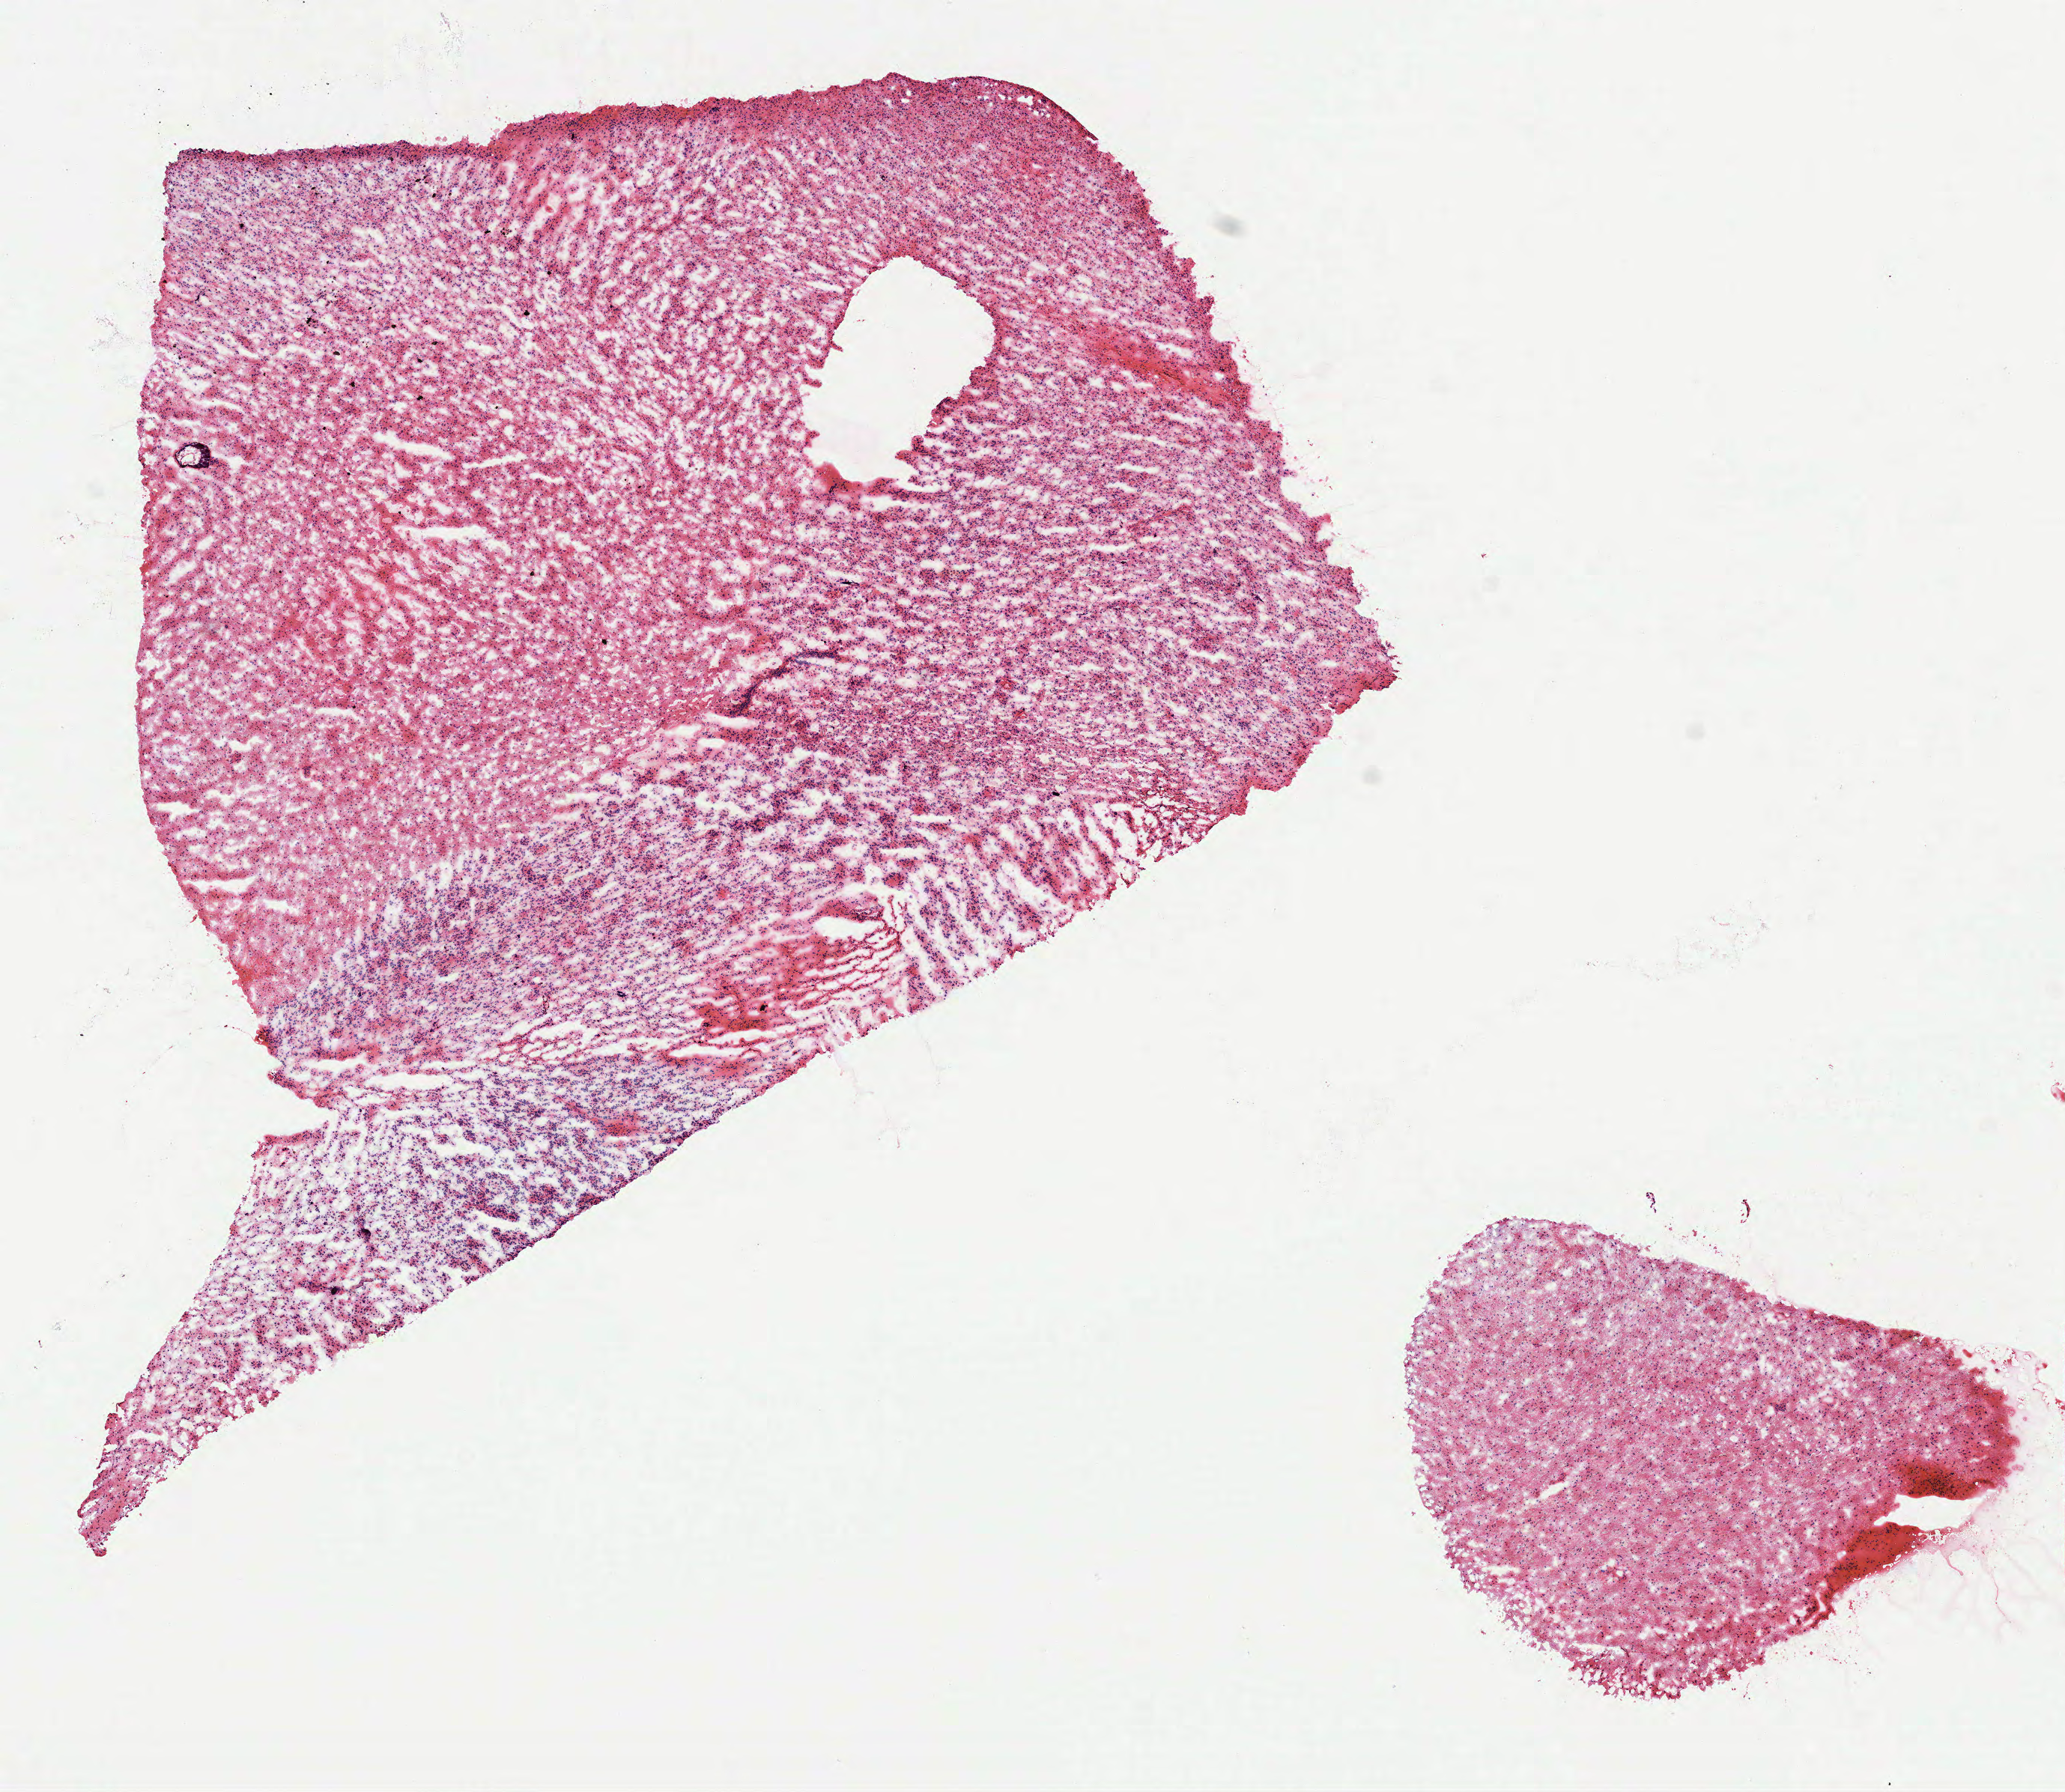
Hematoxylin and eosin (H&E) stained whole-slide image, a low-resolution overview of the entire scanned area, about 11.1 x 9.7 mm (acquisition: 40x scan), frozen section, primary tumour sample from the brain. Male, age 58 years at initial diagnosis. Histologic grade: G3 (poorly differentiated). Composition of this section per pathologist review: tumour cells 100%, tumour nuclei 75%, normal cells 0%, stromal cells 0%, necrosis 0%.
* laterality: right
* diagnosis: Mixed glioma